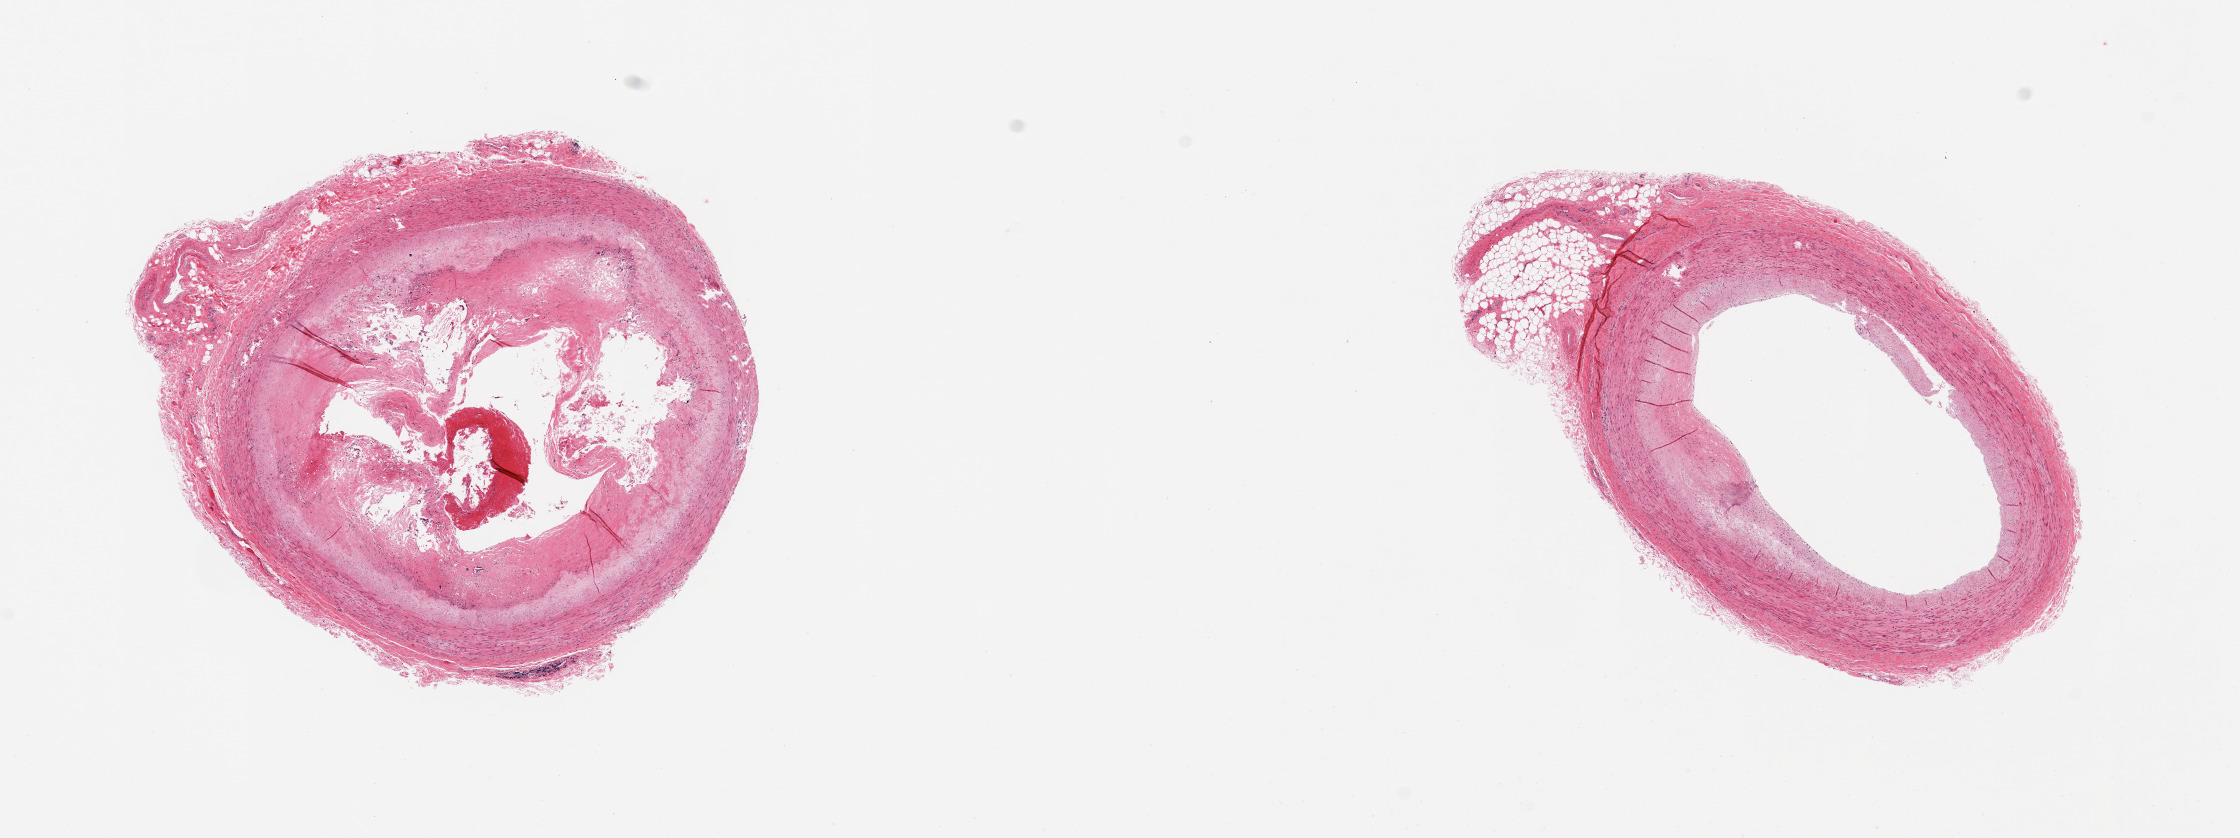
Whole-slide image, hematoxylin and eosin (H&E) stain, brightfield — a low-resolution overview of the entire scanned area, about 17.7 x 6.6 mm (acquisition: 20x scan); PAXgene-fixed, paraffin-embedded tissue; section of coronary artery (target tissue); tissue donor sample.
Pathologist's review note for this sample: 2 pieces; atherosclerosis with organizing thrombus and attached adventitia in one piece and sclerotic plaque in other piece with attached 1mm external fat.